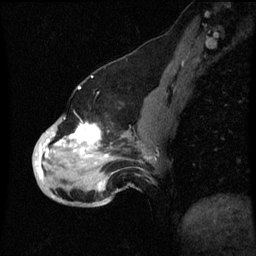
Breast MRI (dynamic contrast-enhanced), one sagittal slice; position 24 of 60 along the scan axis; dynamic contrast-enhanced series, image 2 of 3 at this slice position (ordered by acquisition); 1.5 T; TE 4.2 ms, TR 8.9 ms; 256 × 256 image matrix. Patient: female, 49 years. Case-level facts recorded for this patient, not image findings: setting: breast cancer imaged before/during neoadjuvant chemotherapy; receptor status: HR-positive, HER2-negative.
Outlined on this slice (semi-automatic segmentation, software-assisted and operator-edited):
- analysis volume of interest (the breast-tissue region the enhancement analysis was run in; not a lesion): bounding box <34,116,153,199> (left, top, right, bottom; pixels)
- tumour enhancement mask (voxels above the 70 % enhancement threshold inside the analysis volume of interest): <38,122,101,177>